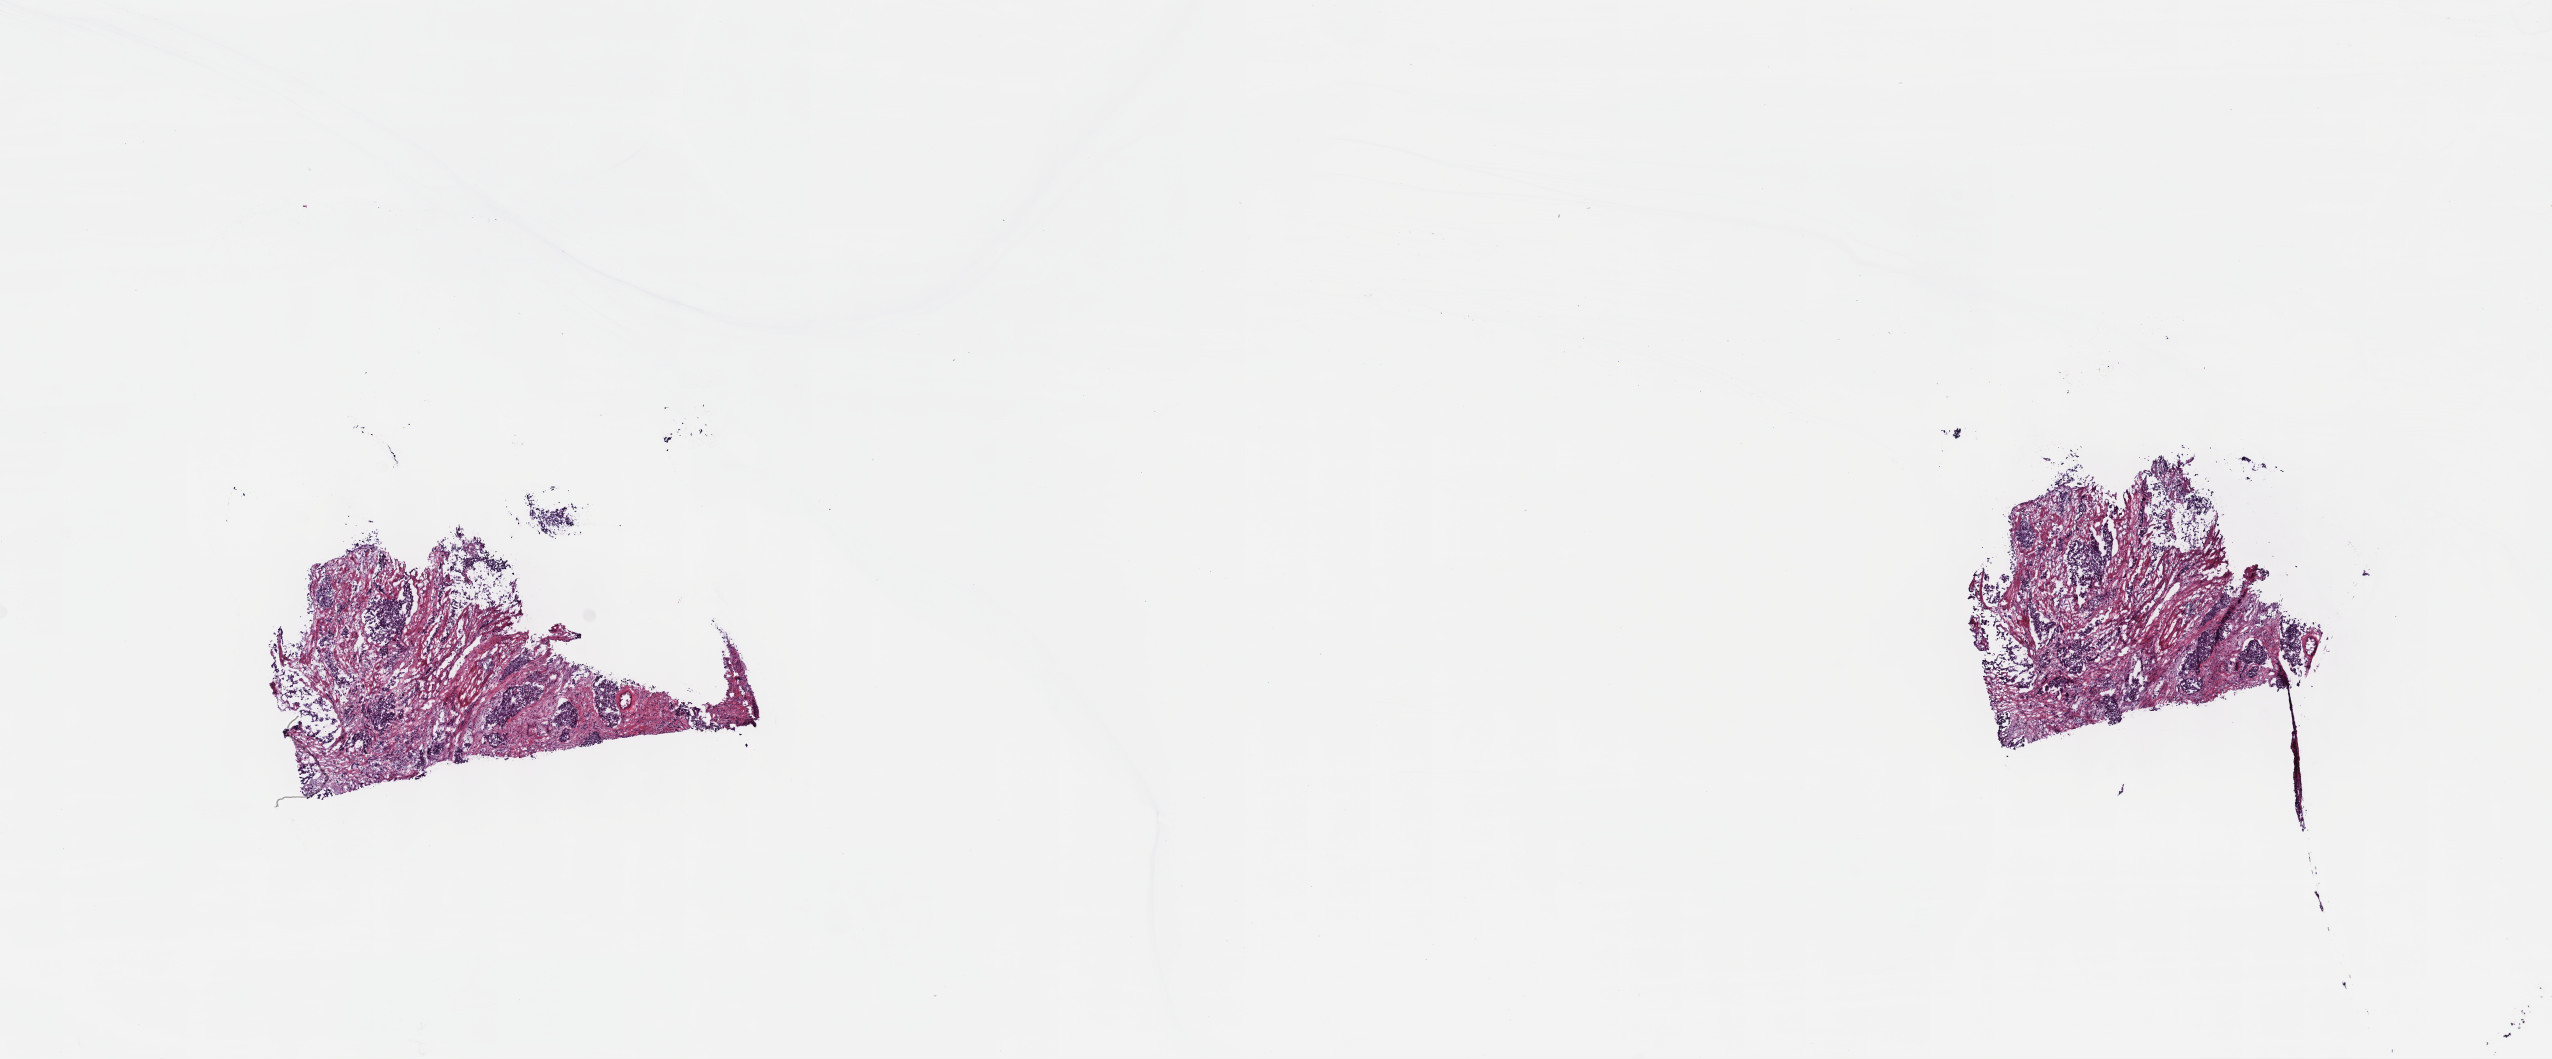
Whole-slide histology image, Hematoxylin and eosin (H&E) stained, whole scanned area (about 20.6 x 8.6 mm, acquisition: 40x scan) shown as a low-resolution overview, frozen section from the top of the tissue portion, primary tumour sample from the bladder. Patient: male, age at initial diagnosis 58 years. Histologic grade: high grade. Composition of this section per pathologist review: tumour cells 100%, tumour nuclei 60%, normal cells 0%, stromal cells 0%, necrosis 0%. Inflammatory infiltration, as recorded: lymphocyte infiltration 2%, monocyte infiltration 0%, neutrophil infiltration 0%.
AJCC pathologic stage: IV. Histologic diagnosis: Transitional cell carcinoma.